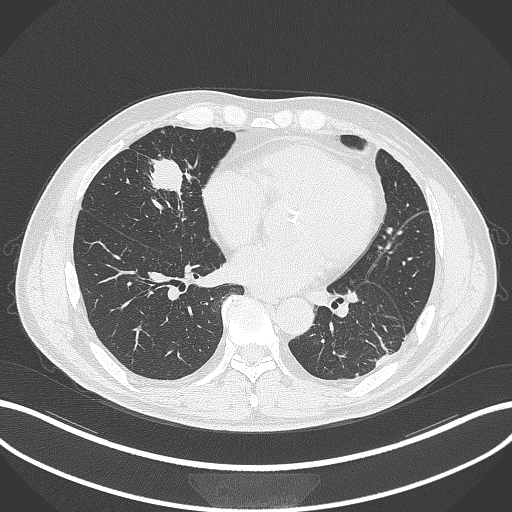
Chest CT, one axial slice; slice 113 of 399 in the series (ordered by position); reconstruction kernel B70f; 120 kVp; lung window (W 1500 / L -600 HU); 1 mm slice thickness; 512 × 512 image matrix, field of view 400 × 400 mm. Patient: male, 59 years. Case-level facts recorded for this patient, not image findings: clinical TNM (as recorded): T2a N1 M0.
Outlined on this slice (bounding box drawn by a radiologist):
- lung tumour (recorded histology: adenocarcinoma): bounding box [x1, y1, x2, y2] px = [146, 157, 194, 200]